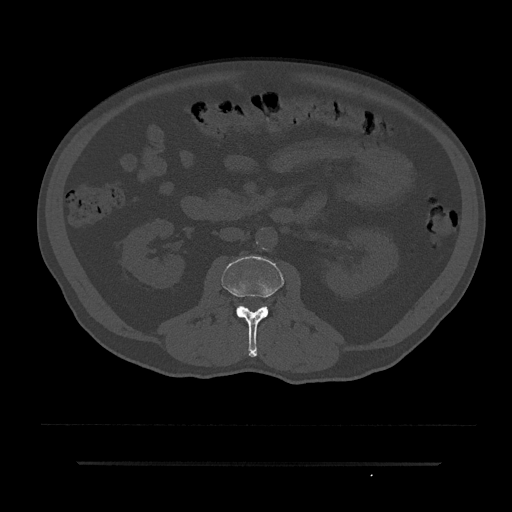
CT including the spine, one axial slice. Slice 59 of 797 in the series (ordered by position). Reconstruction kernel Br40s/3. 120 kVp. Bone window (W 1800 / L 400 HU). 0.5 mm slice thickness. 512 × 512 image matrix, field of view 464 × 464 mm. Patient: male, 59 years. From the clinical record (not read from this slice): primary cancer: bile ducts.
Annotated regions visible in this slice (semi-automatically segmented with operator editing):
- L2 vertebra: bounding box <222,256,284,357> (left, top, right, bottom; pixels)